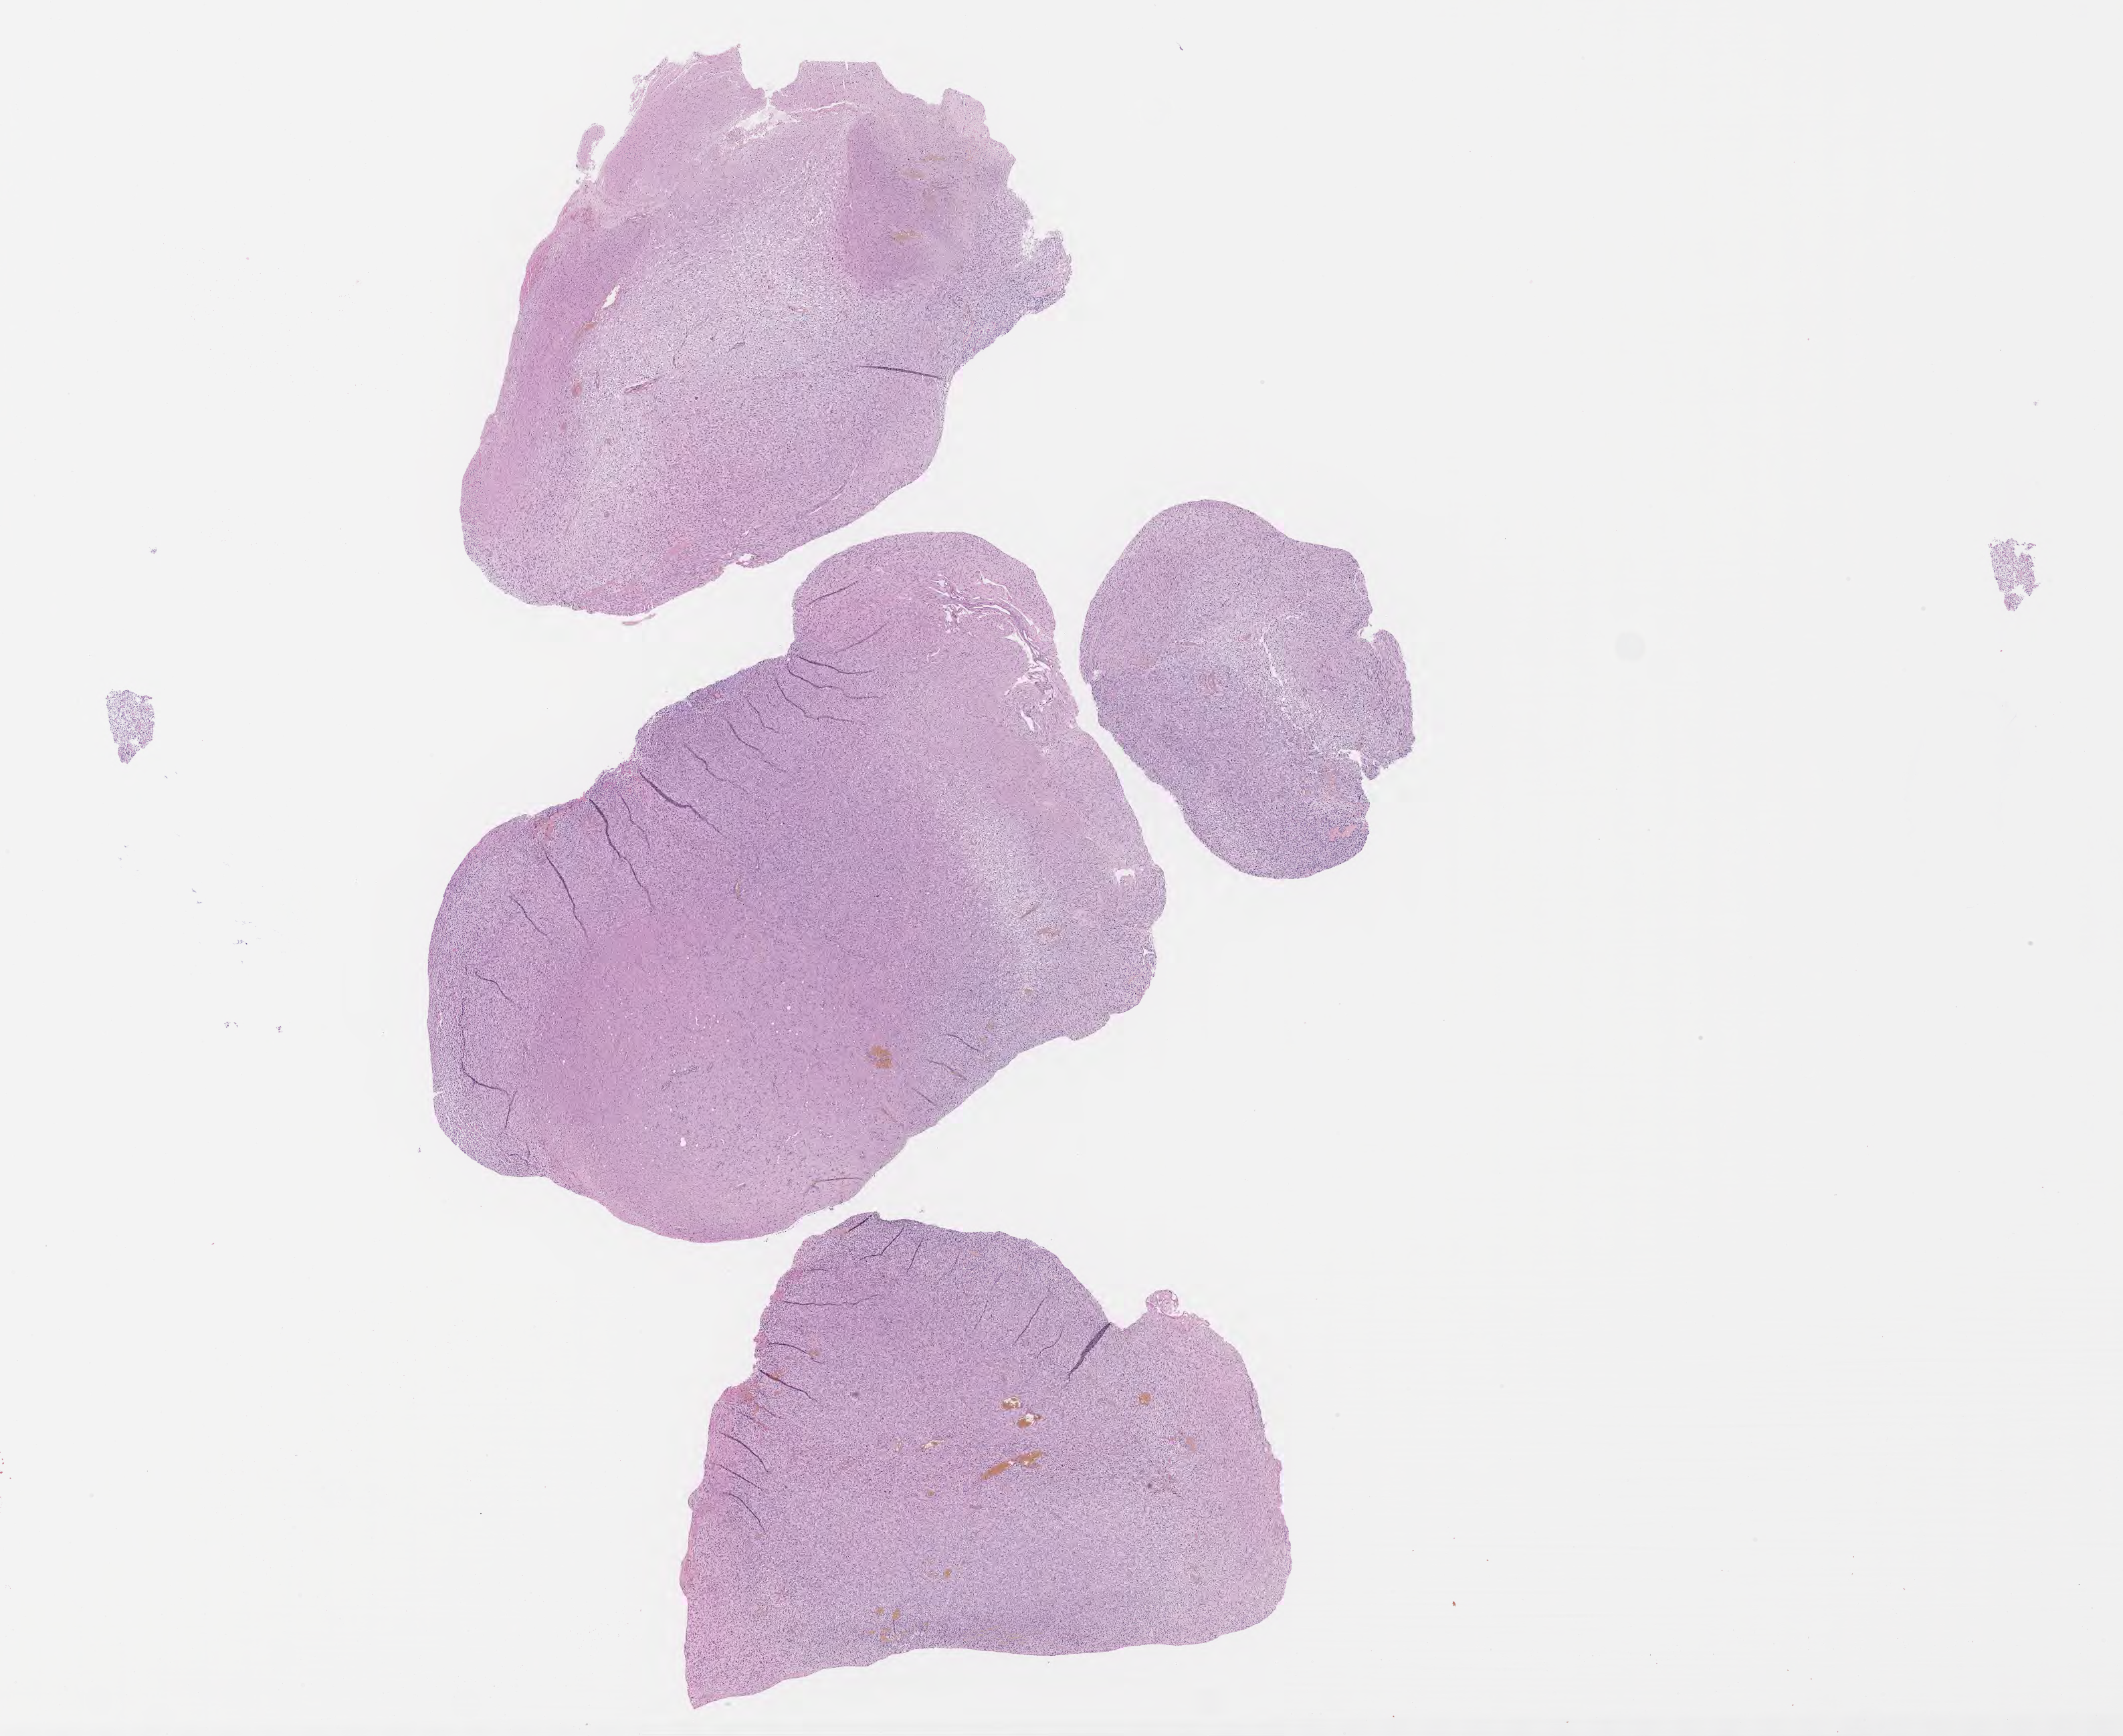
Hematoxylin and eosin (H&E) whole-slide image, shown as a low-resolution overview of the whole scanned area (about 25.7 x 21.0 mm). FFPE section. Primary tumor. Site: brain. Male patient; age at initial diagnosis 66 years. Composition of this section per pathologist review: tumor cells 76%, tumor nuclei 88%, stromal cells 13%, necrosis 1%, normal cells 10%. Inflammatory infiltration, as recorded: lymphocyte infiltration 0%, monocyte infiltration 0%, neutrophil infiltration 0%.
• section: bottom of the tissue portion
• diagnosis: Glioblastoma, NOS